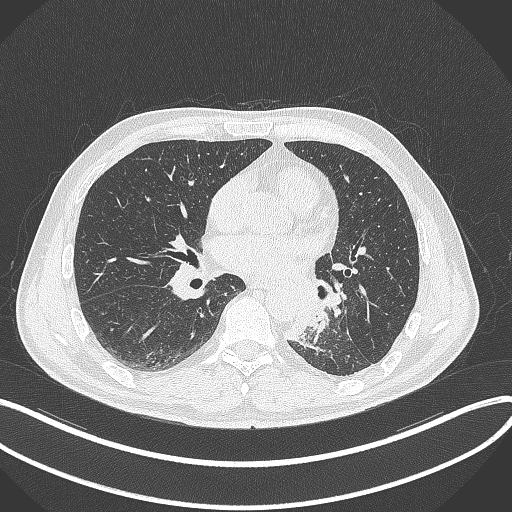
Chest CT, one axial slice. Position 154 of 329 along the scan axis. Reconstruction kernel B70f. 120 kVp. Lung window (W 1500 / L -600 HU). 1 mm slice thickness. 512 × 512 image matrix, field of view 400 × 400 mm. Patient: male, 59 years. Case-level facts recorded for this patient, not image findings: clinical TNM (as recorded): T2a N2 M0.
Structures marked on this image (rectangle marked by the reading radiologist):
- lung tumour (recorded histology: squamous cell carcinoma): bounding box (x1, y1, x2, y2) in pixels: (285, 287, 326, 344)